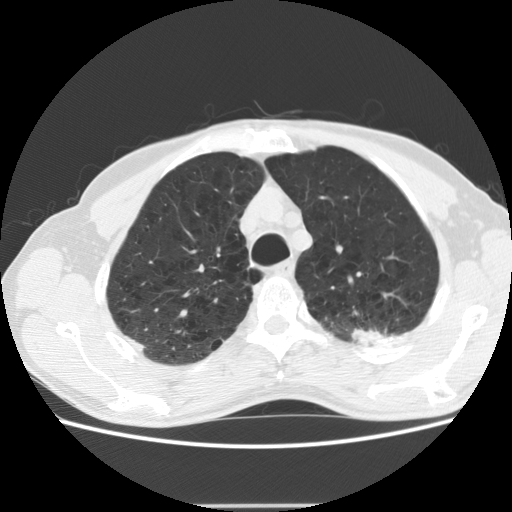
Axial slice from a low-dose chest CT screening exam; baseline screening round; lung window (W 1500 / L -600 HU); 2.5 mm slice thickness; standard (soft-tissue) reconstruction kernel (STANDARD); 120 kVp; slice 38 of 191 in the series. Male, age 64 years at enrolment. Current smoker at enrolment.
Expert-annotated lung lesion, bounding box [x1, y1, x2, y2] px = [341, 290, 425, 359]. The exam's reader record, not a measurement of the box and not confirmed to be the same lesion: non-calcified nodule or mass ≥4 mm, left upper lobe, 27 × 19 mm, poorly defined margins, soft tissue attenuation. Participant outcome: lung cancer diagnosed 23 days after this screen — adenocarcinoma, NOS, left upper lobe, moderately differentiated (G2), stage IA (AJCC 6th edition), 29 mm at pathology.